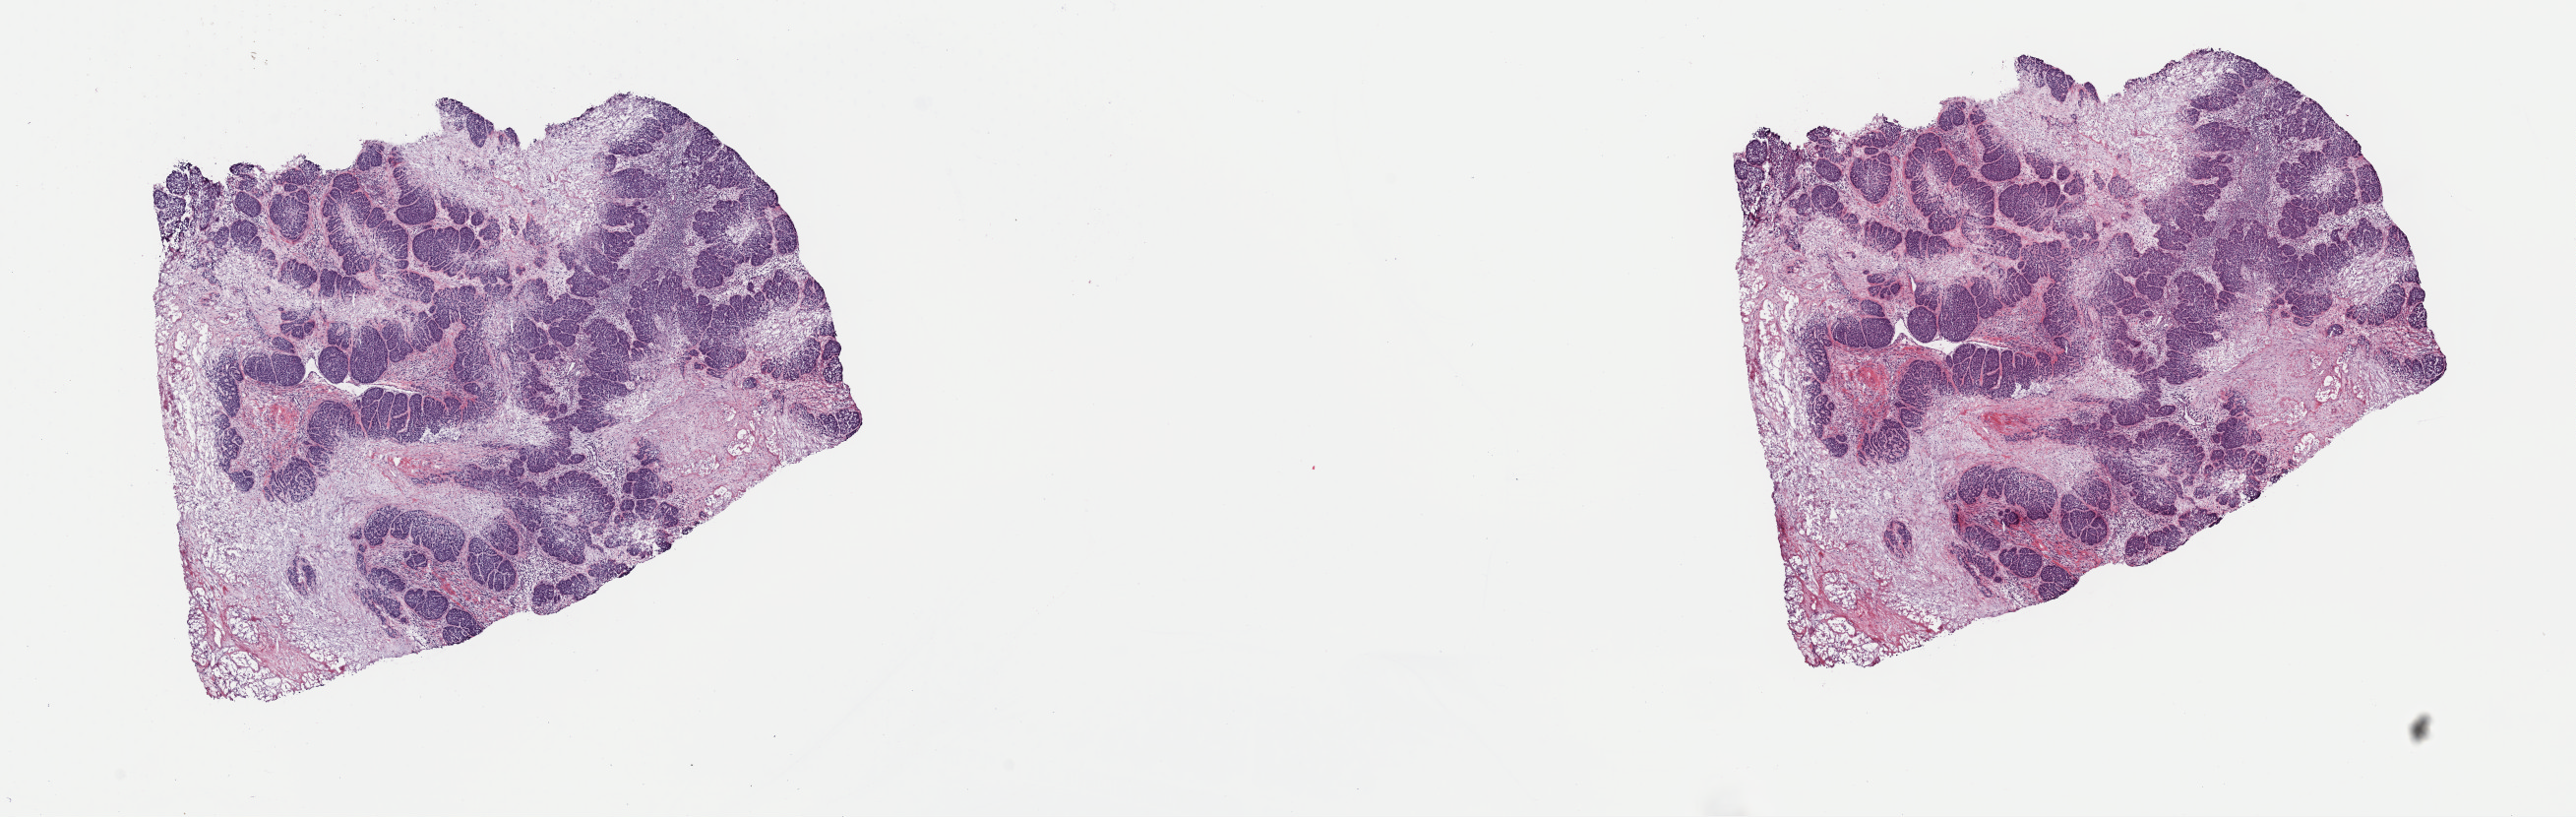
Digitized Hematoxylin and eosin (H&E) stained tissue section (whole slide), low-resolution overview of the scanned area, about 20.7 x 6.6 mm. Frozen section from the top of the tissue portion. Head and neck, primary tumour sample. Patient: male, age at initial diagnosis 56 years. Histologic grade: G3 (poorly differentiated). Slide review estimates, as recorded: tumour cells 50%, tumour nuclei 80%, normal cells 0%, stromal cells 48%, necrosis 2%. Infiltration values recorded for this section: lymphocyte infiltration 10%, monocyte infiltration 0%, neutrophil infiltration 0%.
- diagnosis: Squamous cell carcinoma, NOS (floor of mouth, NOS)
- AJCC pathologic stage: IVA (6th edition)